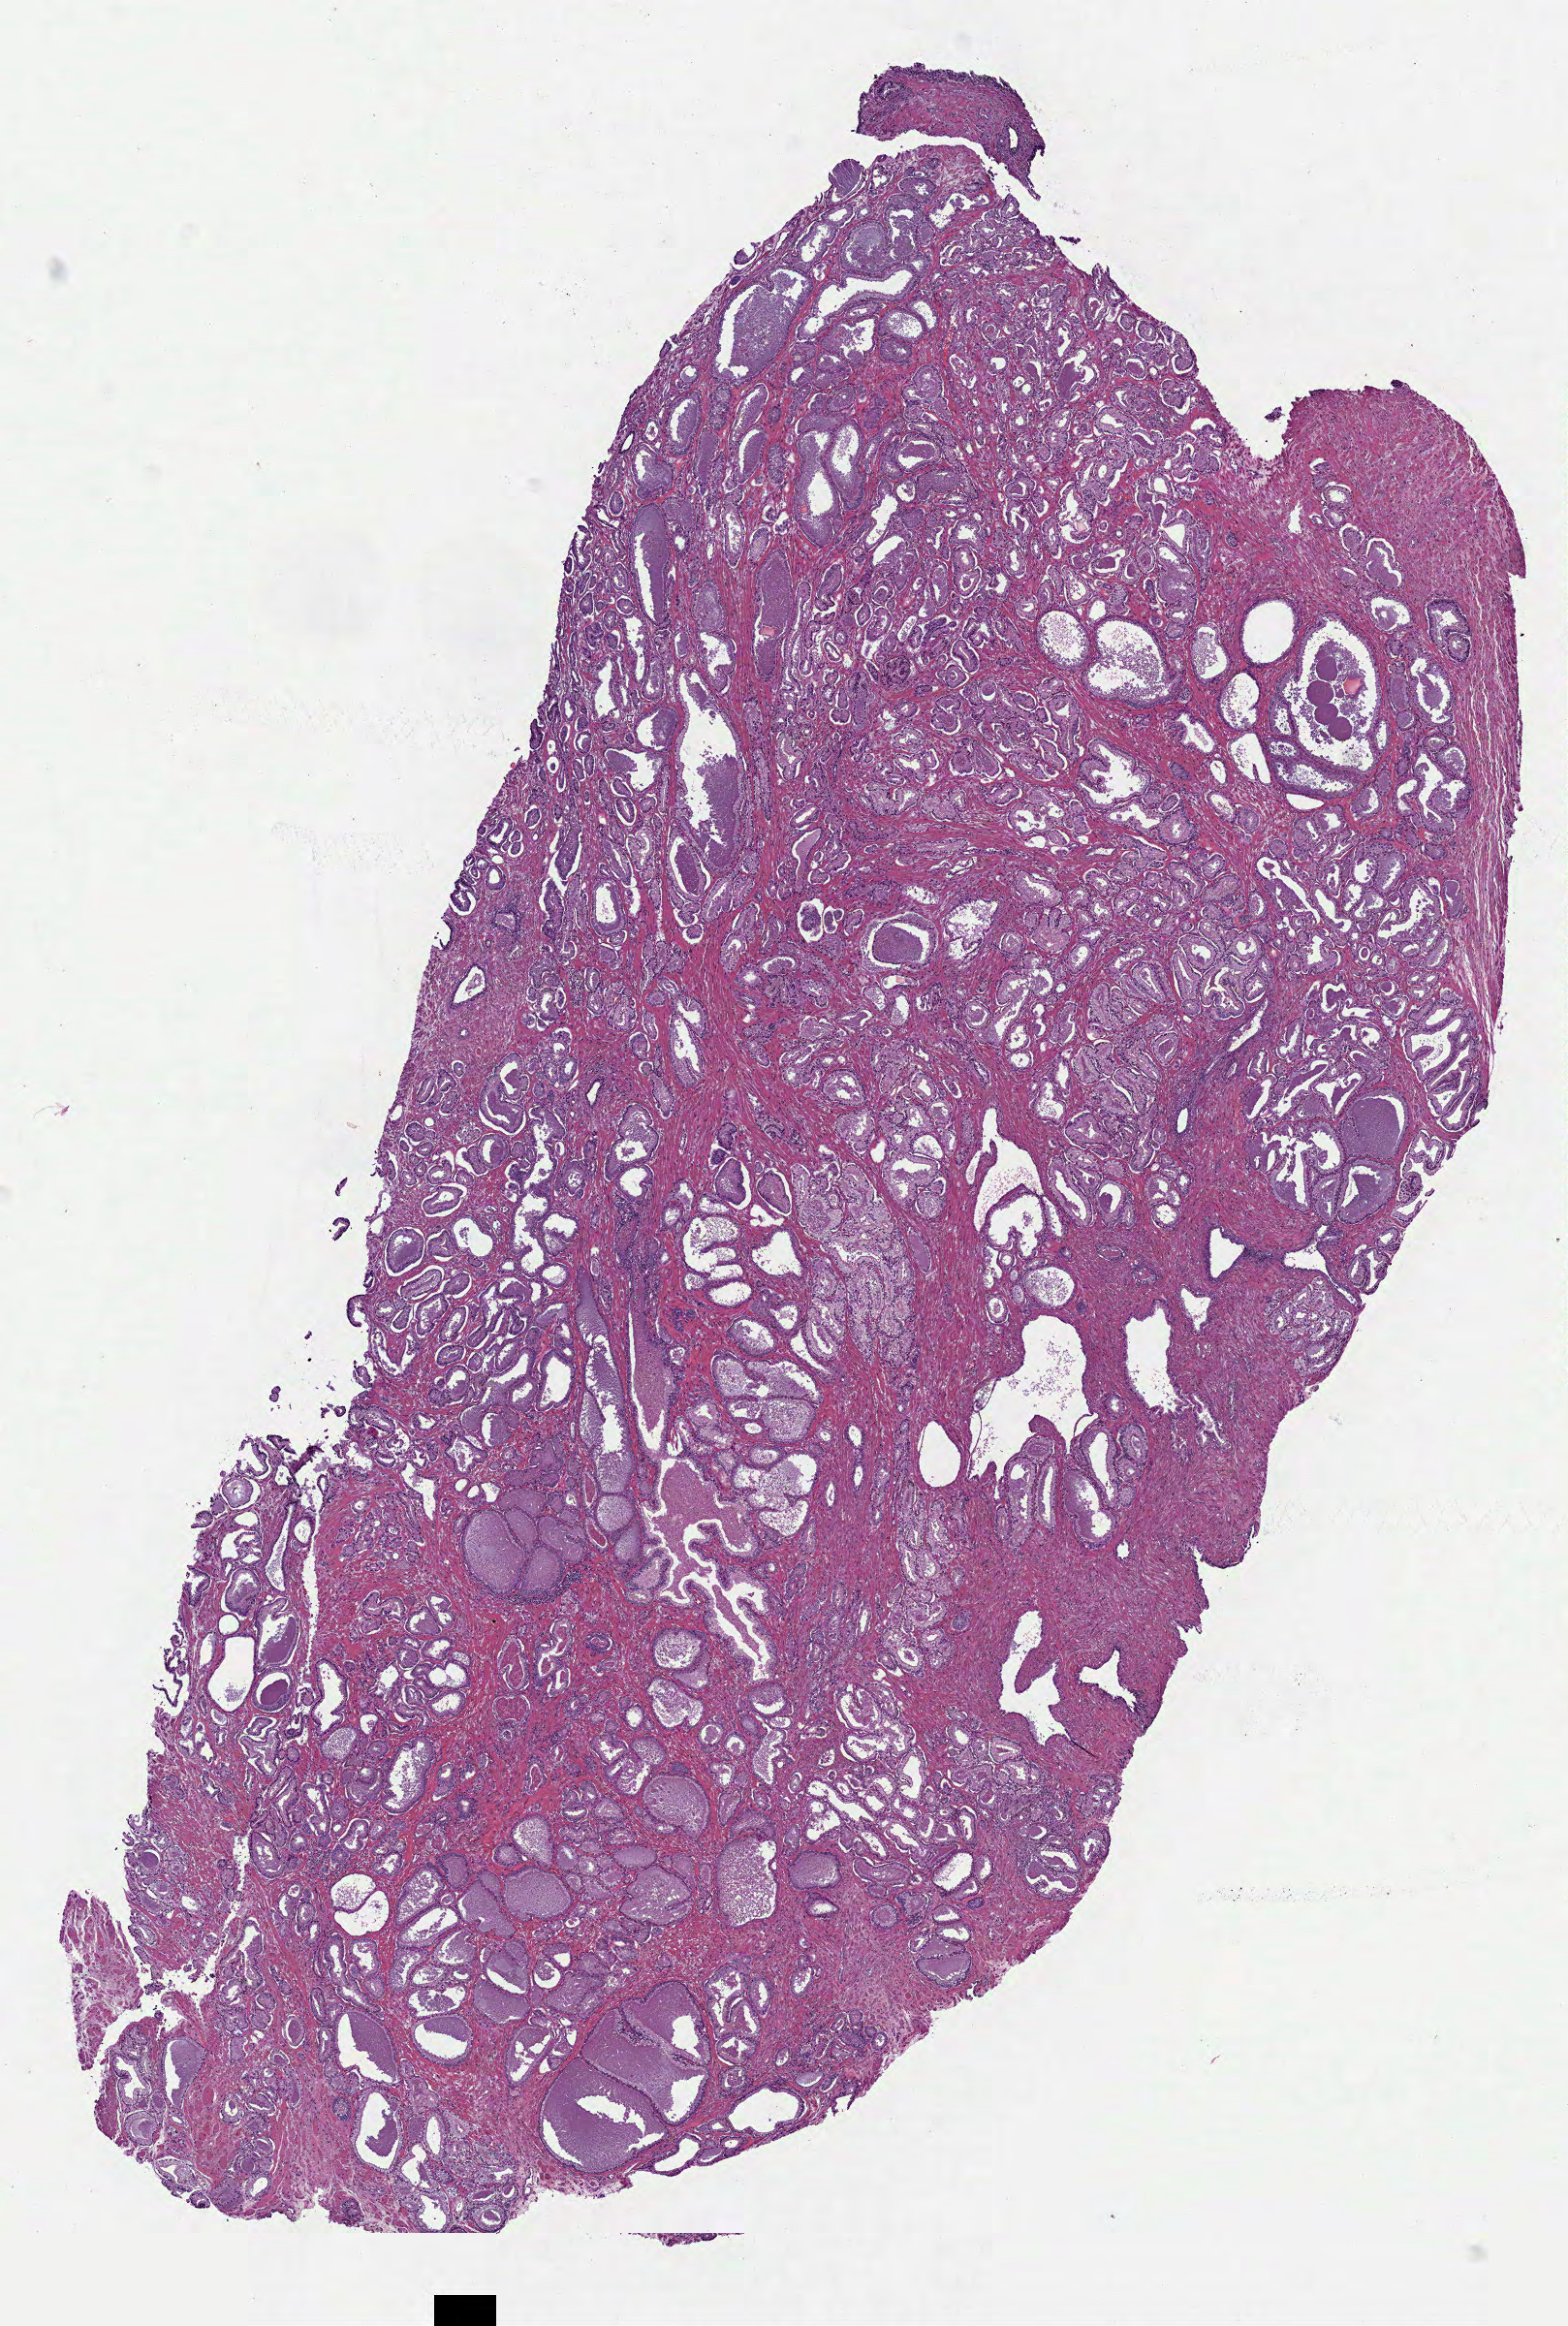
Hematoxylin and eosin (H&E) stained whole-slide image, low-resolution overview of the scanned area, about 6.5 x 9.7 mm; formalin-fixed paraffin-embedded (FFPE) diagnostic section; sample: primary tumour, prostate. Male patient; age at initial diagnosis 50 years. Gleason score: 7 (3+4).
Laterality: left. Pathologic diagnosis: Acinar cell carcinoma.